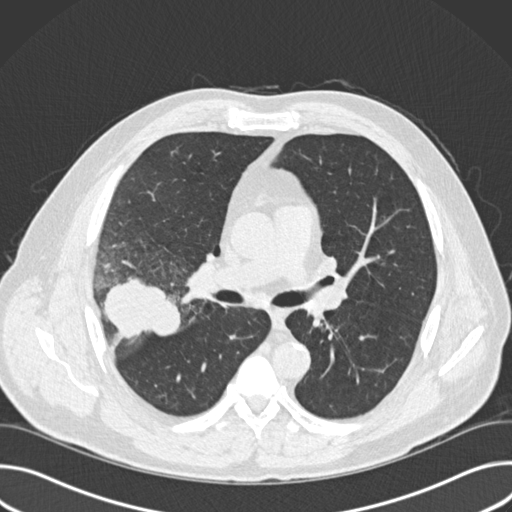
Low-dose screening chest CT, one axial slice; position 97 of 157 along the scan axis; reconstruction kernel B30f; 120 kVp; lung window (W 1500 / L -600 HU); 2 mm slice thickness; 512 × 512 image matrix, field of view 380 × 380 mm.
Annotated regions visible in this slice (outlined manually by an expert reader):
- lesion 1 (tumor, upper lobe of right lung): bounding box (x1, y1, x2, y2) in pixels: (102, 277, 181, 339)